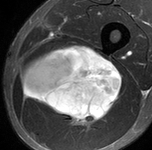
MRI of an extremity soft-tissue mass, one axial slice; slice 58 of 90 in the series (ordered by position); STIR; MR volume resampled by the dataset authors to the PET/CT grid (not the native acquisition matrix); 3.27 mm slice thickness; 152 × 150 image matrix, field of view 148 × 146 mm. Male patient. From the clinical record (not read from this slice): histological type: undifferentiated pleomorphic liposarcoma; grade: high; site of the primary tumour: left thigh.
Outlined on this slice (expert contour drawn on MRI and transferred to this co-registered scan by the dataset authors):
- gross tumour volume including surrounding oedema: bounding box <20,44,124,127> (left, top, right, bottom; pixels)
- gross tumour volume (mass): <20,44,124,125>